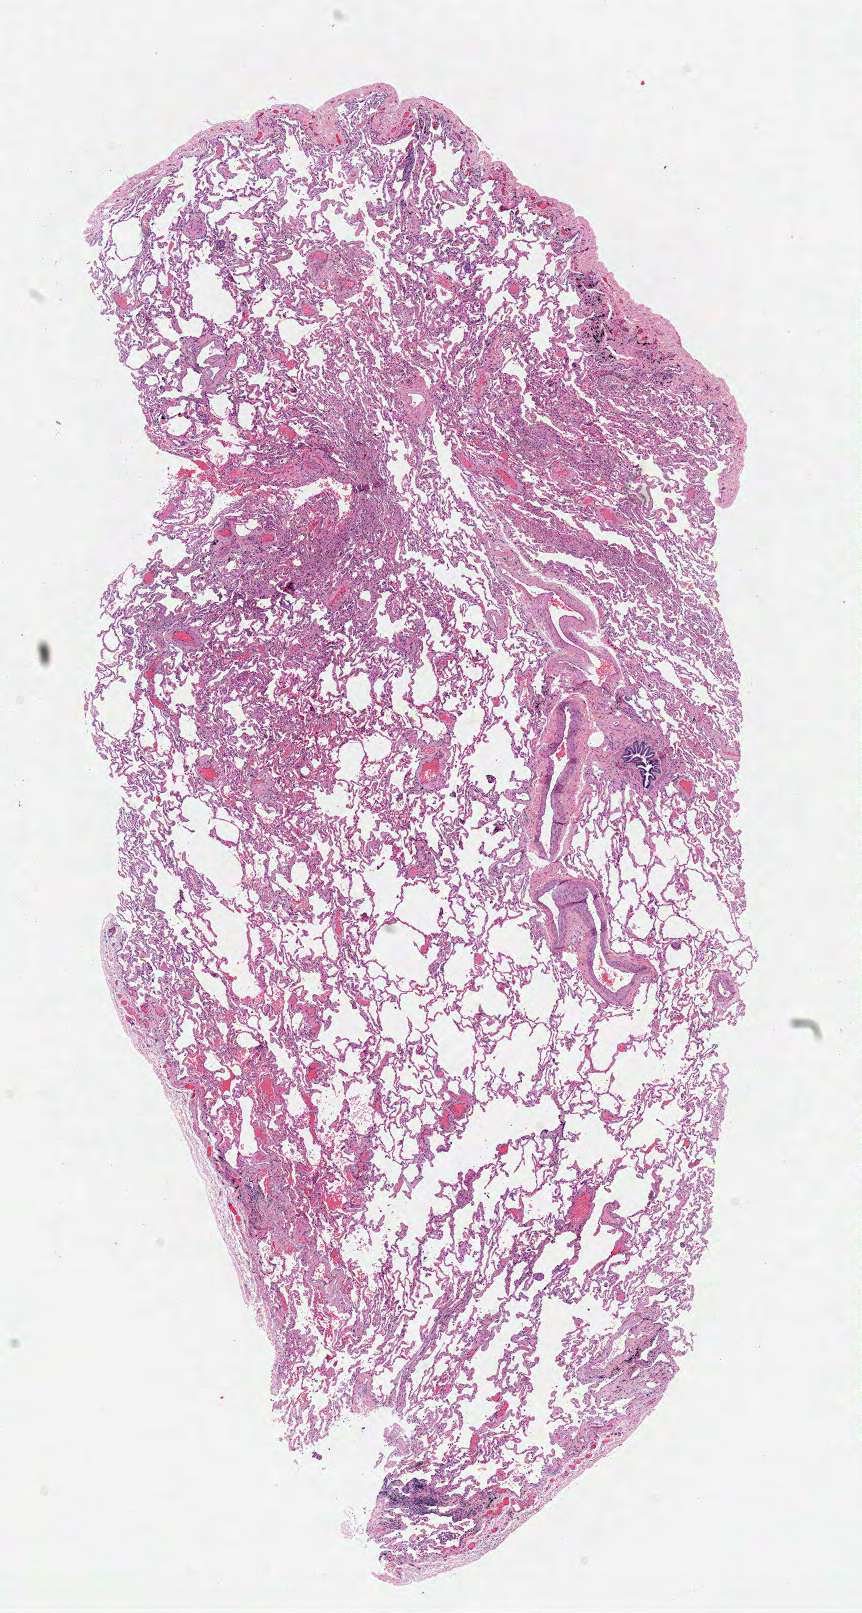
Whole-slide histology image, H&E, shown as a low-resolution overview of the whole scanned area (about 6.8 x 12.7 mm, slide scanned at 40x); frozen section from the top of the tissue portion; solid tissue normal (non-tumour tissue) sample from the lung. Female, age 75 years at initial diagnosis.
- this section: solid tissue normal sample (biorepository sample class)
- patient diagnosis: Adenocarcinoma, NOS (upper lobe, lung)